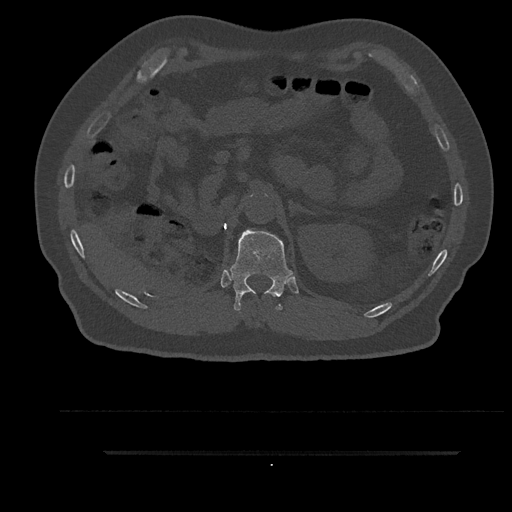
CT including the spine, one axial slice. Position 252 of 797 along the scan axis. 120 kVp. Bone window (W 1800 / L 400 HU). 0.5 mm slice thickness. 512 × 512 image matrix. Patient: male, 63 years. Case-level facts recorded for this patient, not image findings: primary cancer: renal; vertebrae with lytic lesions (as recorded): T8.
Structures marked on this image (semi-automatic segmentation, software-assisted and operator-edited):
- T12 vertebra: bounding box (x1, y1, x2, y2) in pixels: (227, 229, 293, 311)